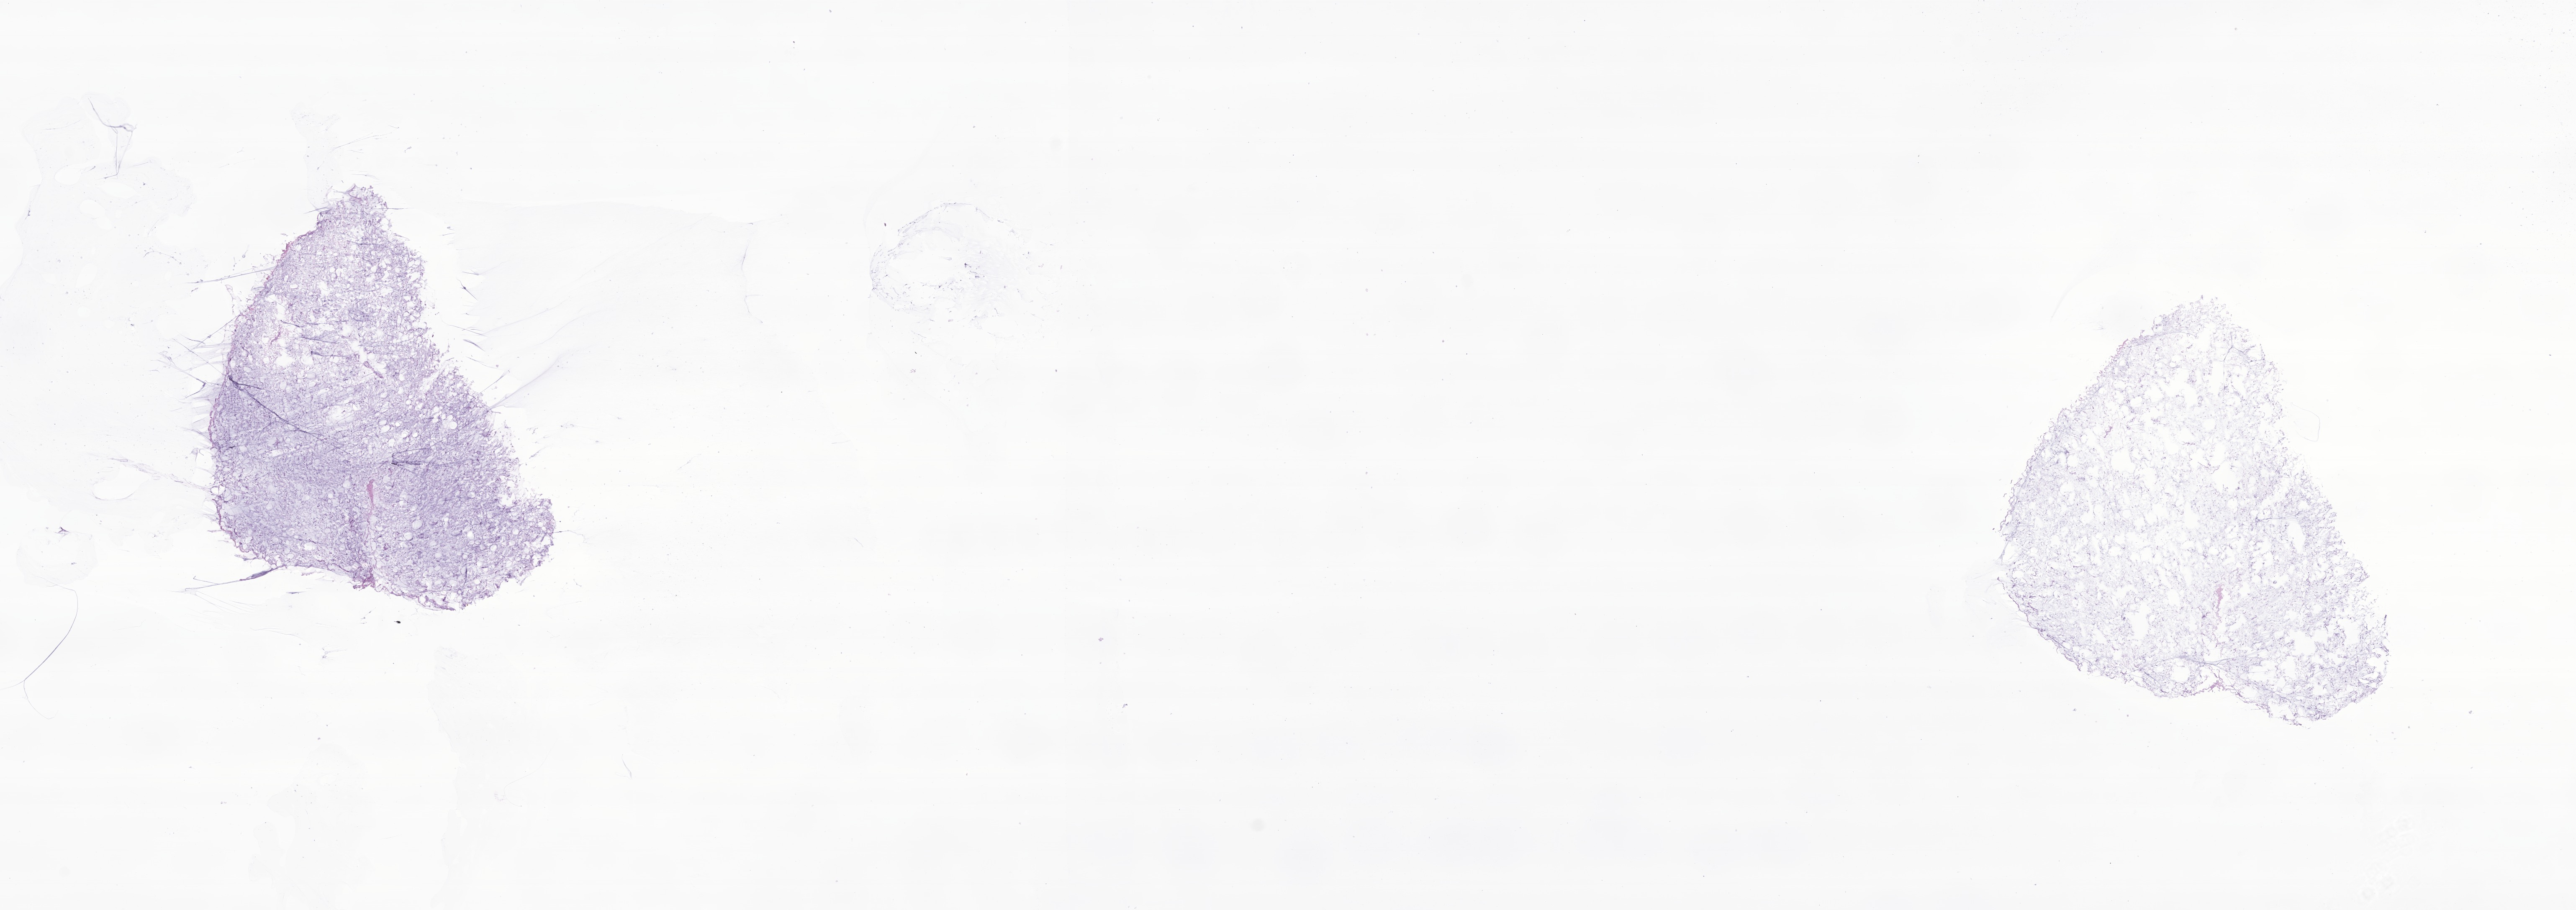
Whole-slide image, haematoxylin and eosin stain of tumor tissue from the soft tissue of upper extremity — low-resolution overview of the scanned area, about 25.9 x 9.2 mm; frozen section. Female patient, age 342 days.
• recorded diagnosis: Neoplasm, uncertain whether benign or malignant